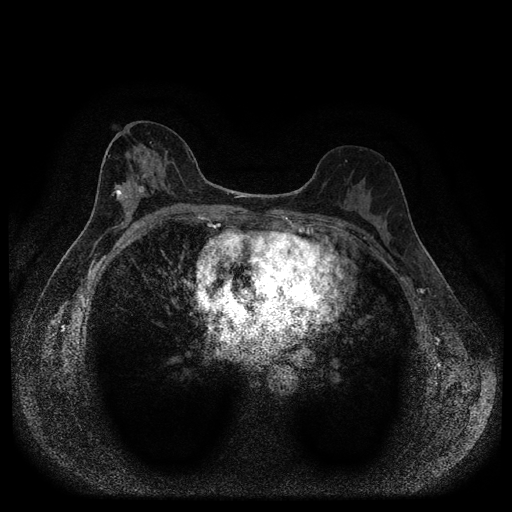
Breast MRI (dynamic contrast-enhanced, multi-phase), one axial slice; slice 52 of 116 in the series (ordered by position); dynamic contrast-enhanced series, time point 2 of 5 at this slice position (early post-contrast); 1.5 T; TE 2.7 ms, TR 5.4 ms; 512 × 512 image matrix. Female patient, age 49 years.
Structures marked on this image (semi-automatically segmented with operator editing):
- breast lesion (labelled 'tumour' in the annotation; benign lesions carry a separate 'benign' label): bounding box [x1, y1, x2, y2] px = [110, 185, 126, 202]